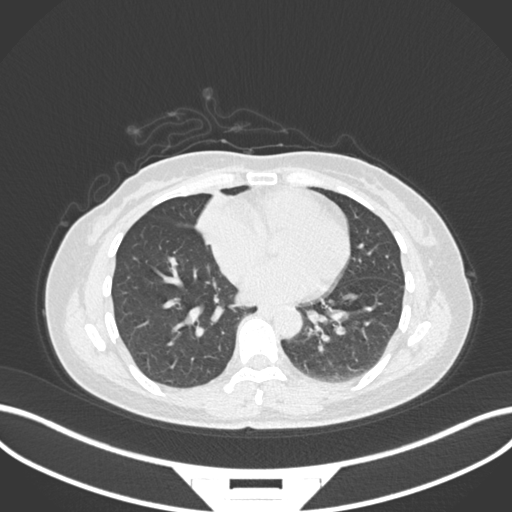
Chest CT, one axial slice; reconstruction kernel B30f; 120 kVp; lung window (W 1500 / L -600 HU); 1 mm slice thickness; 512 × 512 image matrix, field of view 400 × 400 mm. Patient: female, 43 years. Case-level facts recorded for this patient, not image findings: clinical TNM (as recorded): T1c N3 M1.
Structures marked on this image (bounding box drawn by a radiologist):
- lung tumour (recorded histology: adenocarcinoma): box from (x=191, y=190) to (x=221, y=246) px